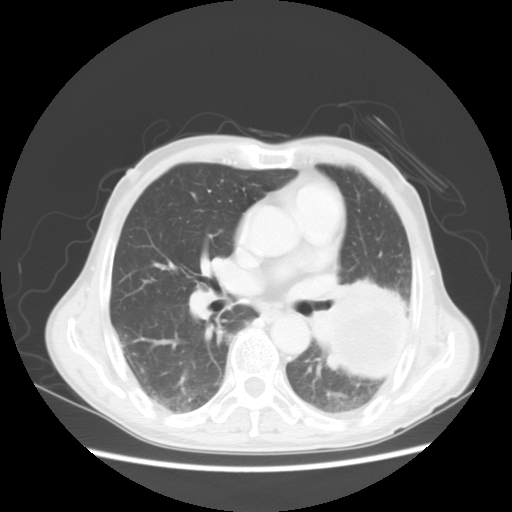
Chest CT, one axial slice. Slice 27 of 51 in the series (ordered by position). 120 kVp. Lung window (W 1500 / L -600 HU). 512 × 512 image matrix, field of view 360 × 360 mm. Male patient, age 64 years. From the clinical record (not read from this slice): clinical TNM (as recorded): T4 N0 M0; histopathological grade: G2-3.
Annotated regions visible in this slice (bounding box drawn by a radiologist):
- lung tumour (recorded histology: squamous cell carcinoma): bounding box [x1, y1, x2, y2] px = [315, 262, 416, 390]